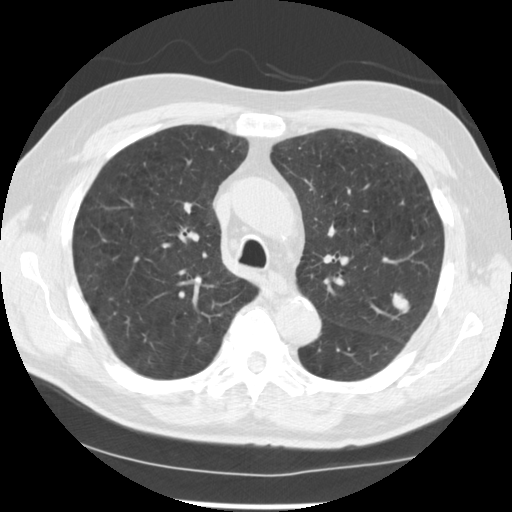
Axial slice from a low-dose chest CT screening exam. Baseline annual screen. Lung window (W 1500 / L -600 HU). Standard (soft-tissue) reconstruction kernel (STANDARD). Slice 170 of 249 in the series. 512 × 512 image matrix. Male, age 71 years at enrolment. Current smoker at enrolment.
• Lesion marked by an expert reader, box from (x=381, y=283) to (x=424, y=328) px.
• The screening reader recorded 2 non-calcified nodules or masses ≥4 mm on this exam; which of them this box marks is not recorded.
• Participant outcome: lung cancer diagnosed 37 days after this screen — adenocarcinoma, NOS, left upper lobe, poorly differentiated (G3), stage IIIB (AJCC 6th edition), 25 mm at pathology.